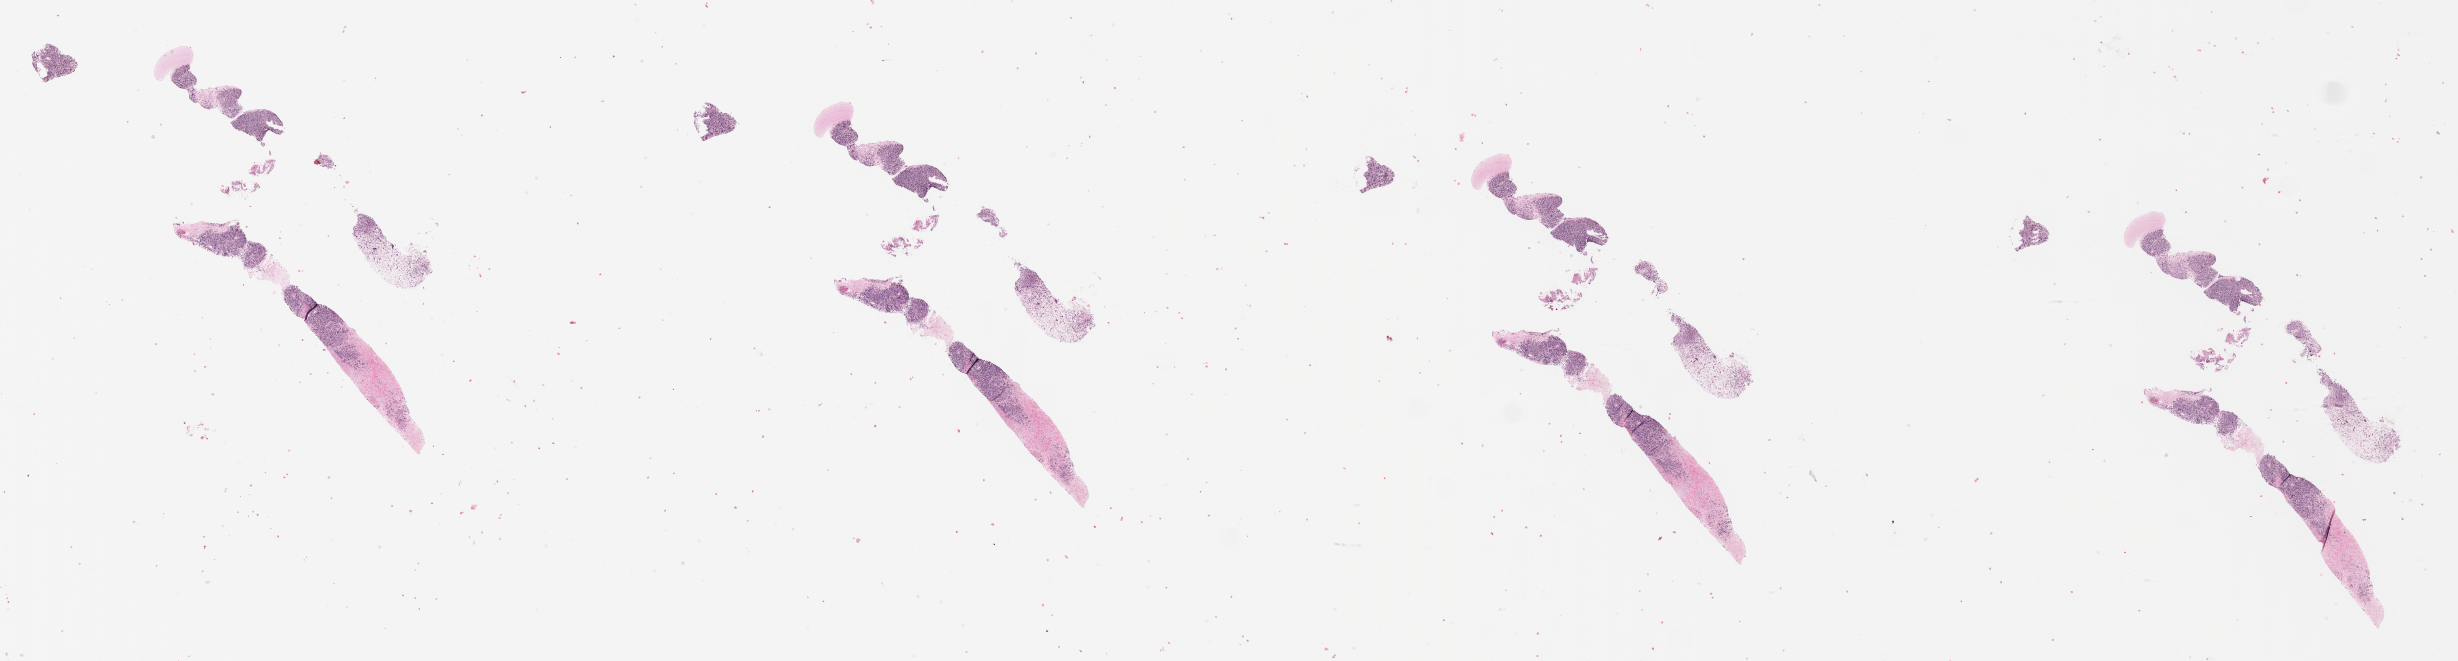
Hematoxylin and eosin (H&E) whole-slide image of tumor tissue — low-resolution overview of the scanned area, about 39.8 x 10.7 mm. Formalin-fixed, paraffin-embedded (FFPE) tissue. Sample anatomic site: pelvis. Male patient, age at diagnosis 4.8 years.
- diagnosis: rhabdomyosarcoma; histological classification: embryonal rhabdomyosarcoma
- metastatic status at presentation (as recorded): metastatic (confirmed)
- stage (as recorded): 4